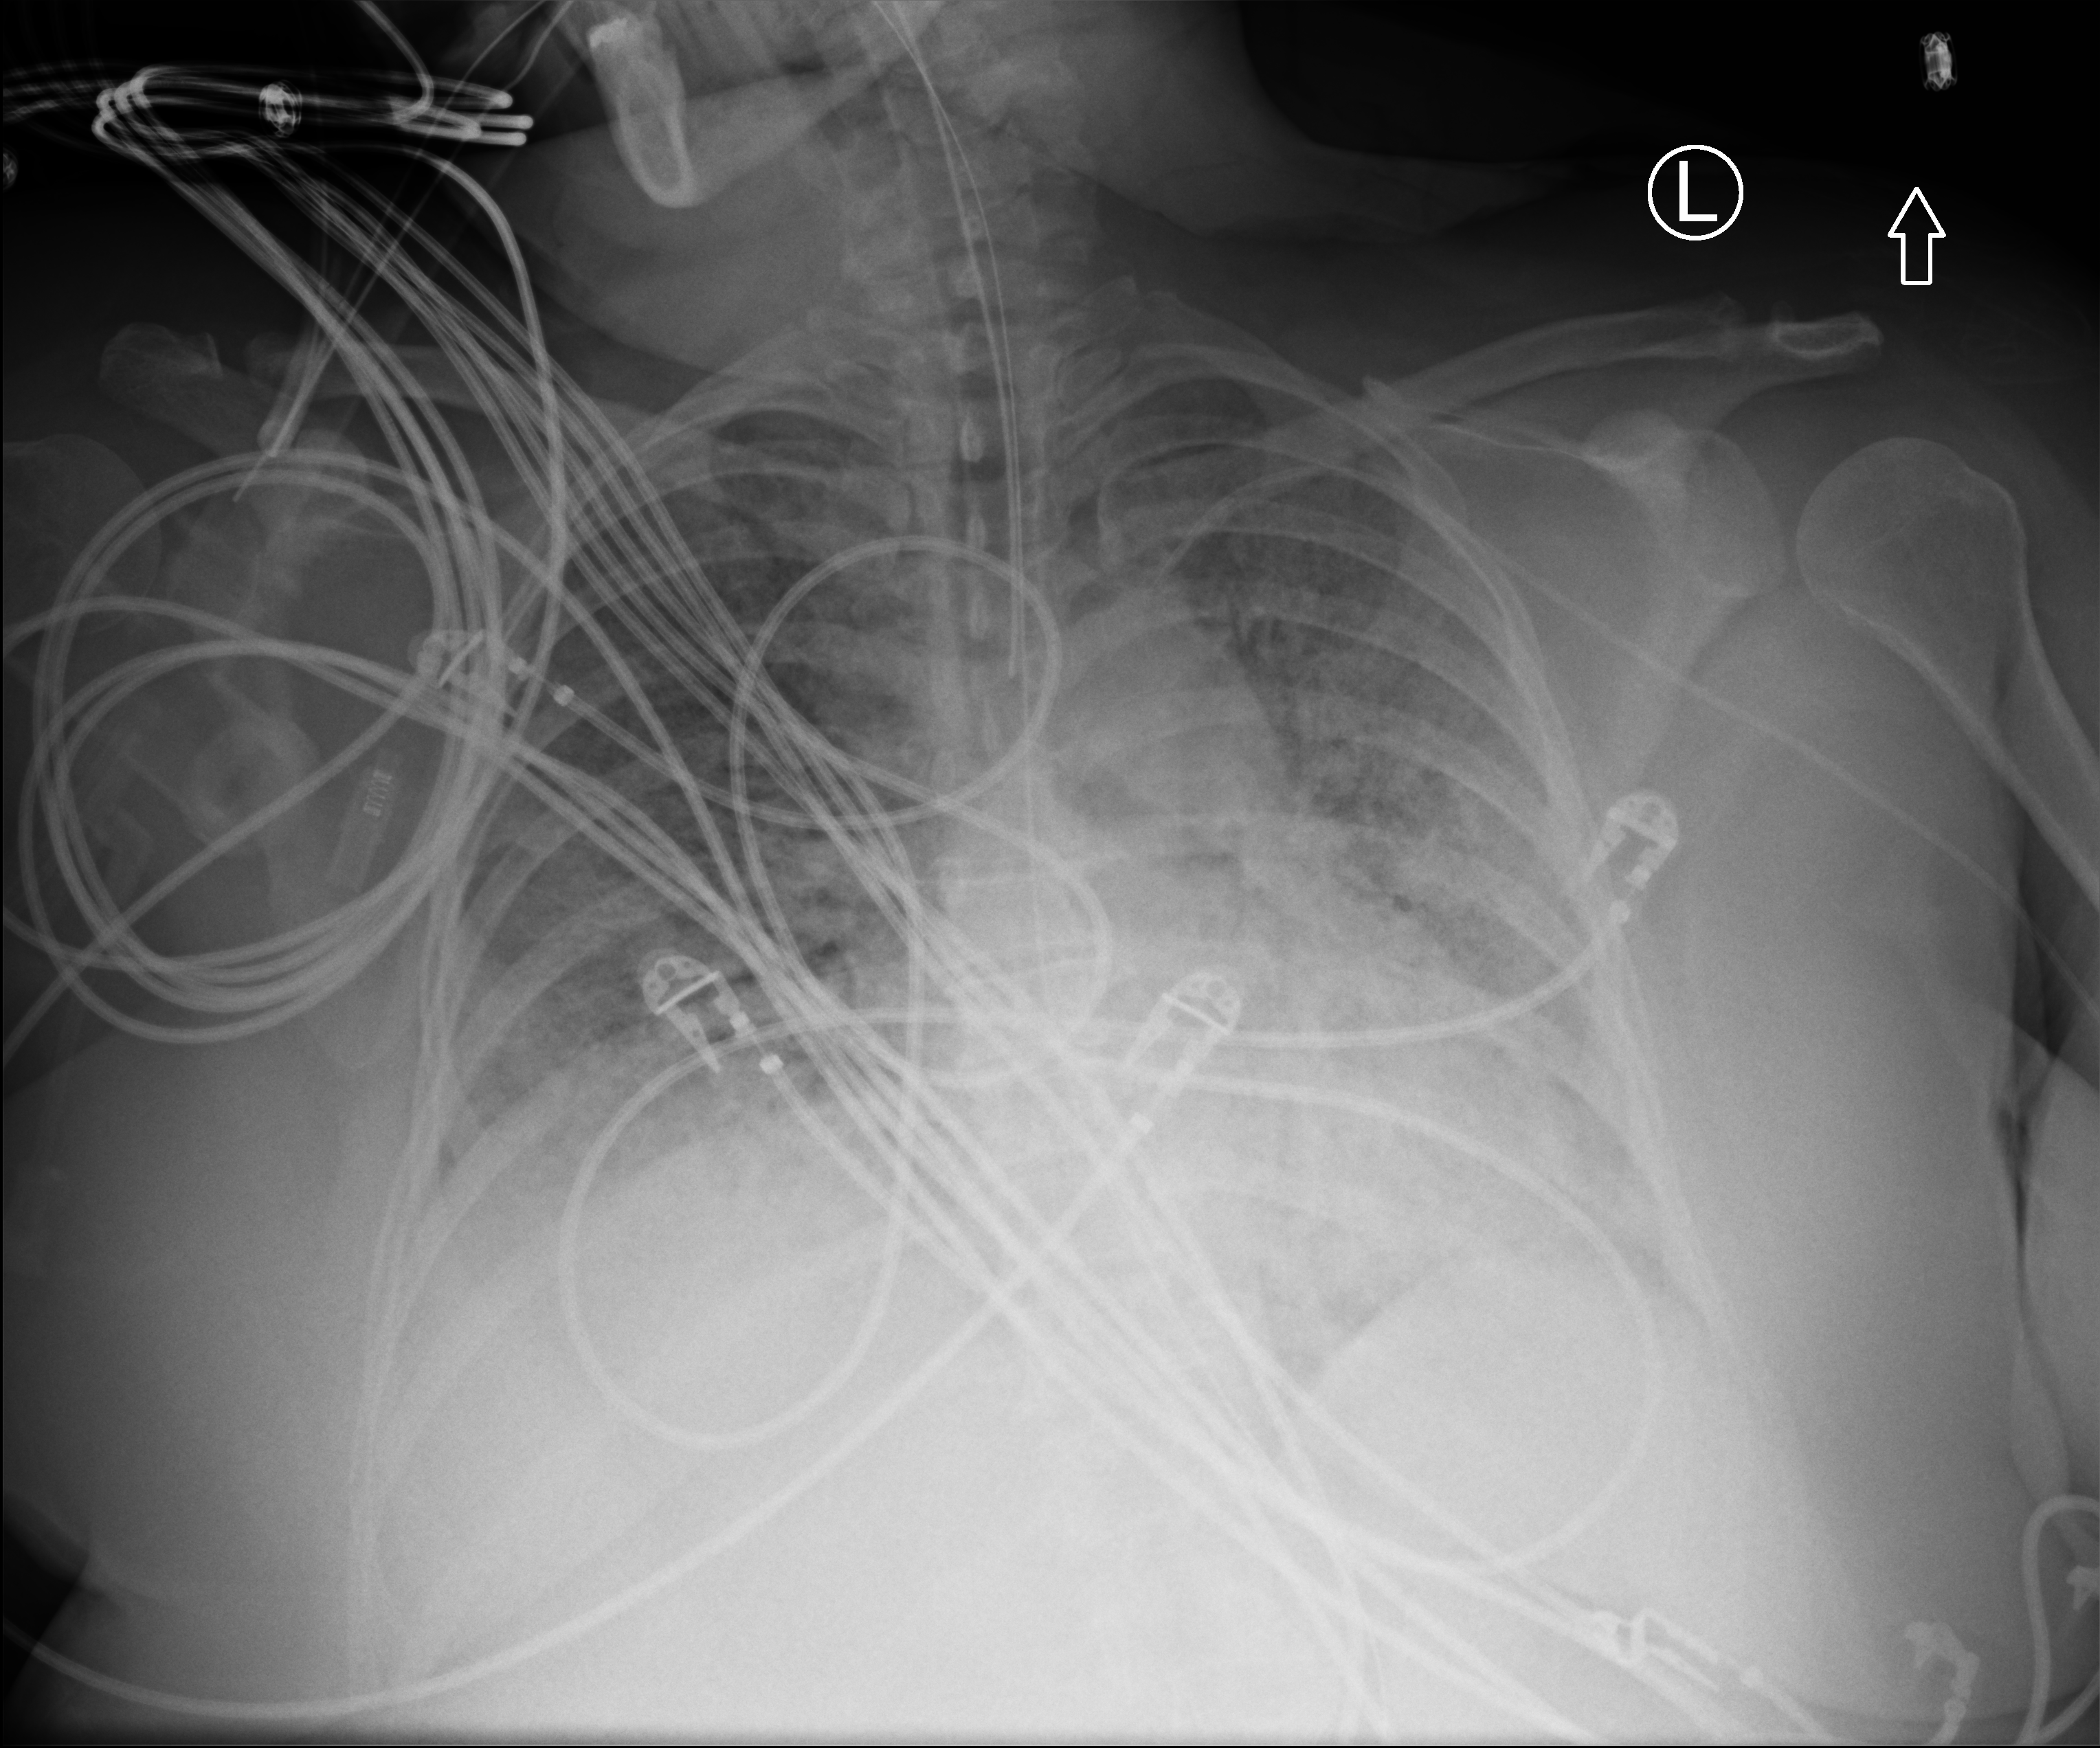
Bedside chest radiograph (computed radiography), anteroposterior (AP) projection. Patient hospitalised with COVID-19; female, aged 18–59 years.
Hospital-stay facts (about this admission, not read from this image; timing relative to this image not recorded):
- mechanically ventilated during this hospital stay: yes
- other chronic lung disease (admission record): no
- admitted to intensive care during this hospital stay: yes